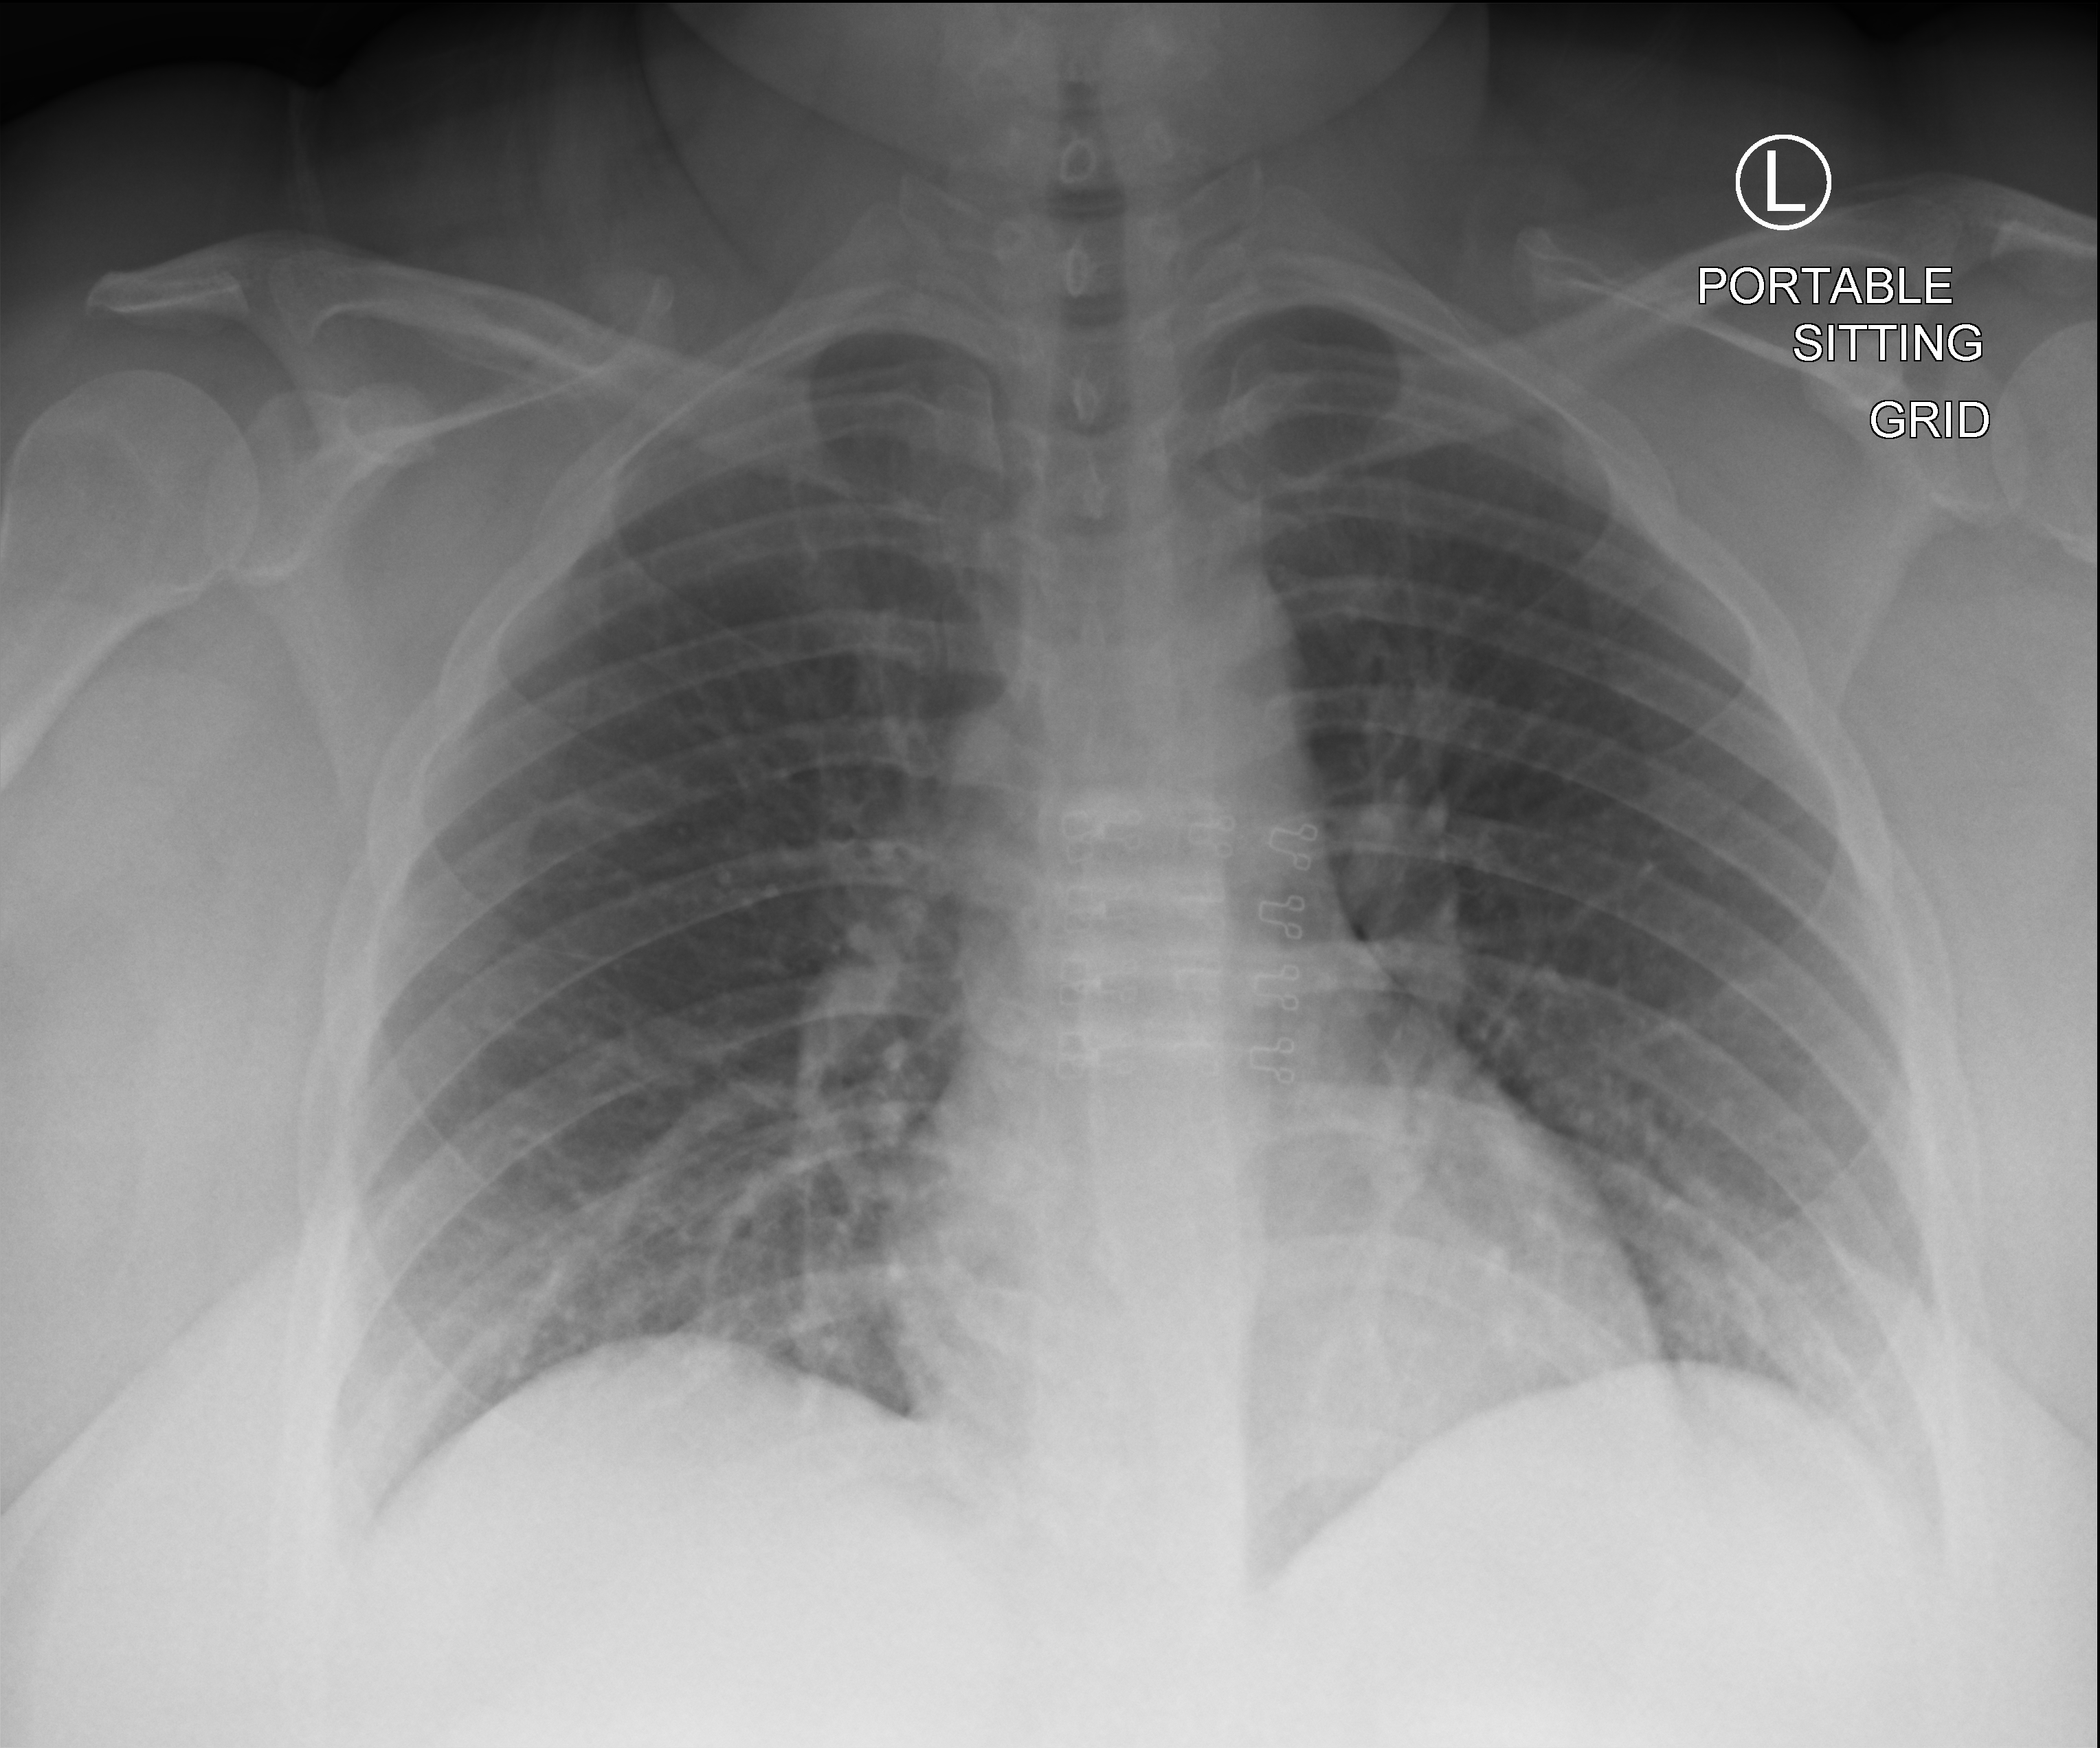
Portable chest radiograph. Patient hospitalised with COVID-19; female, aged 18–59 years.
From the hospital-stay record, not from the radiograph (when in the stay this image was taken is not recorded):
- admitted to intensive care during this hospital stay: no
- chronic kidney disease (admission record): no